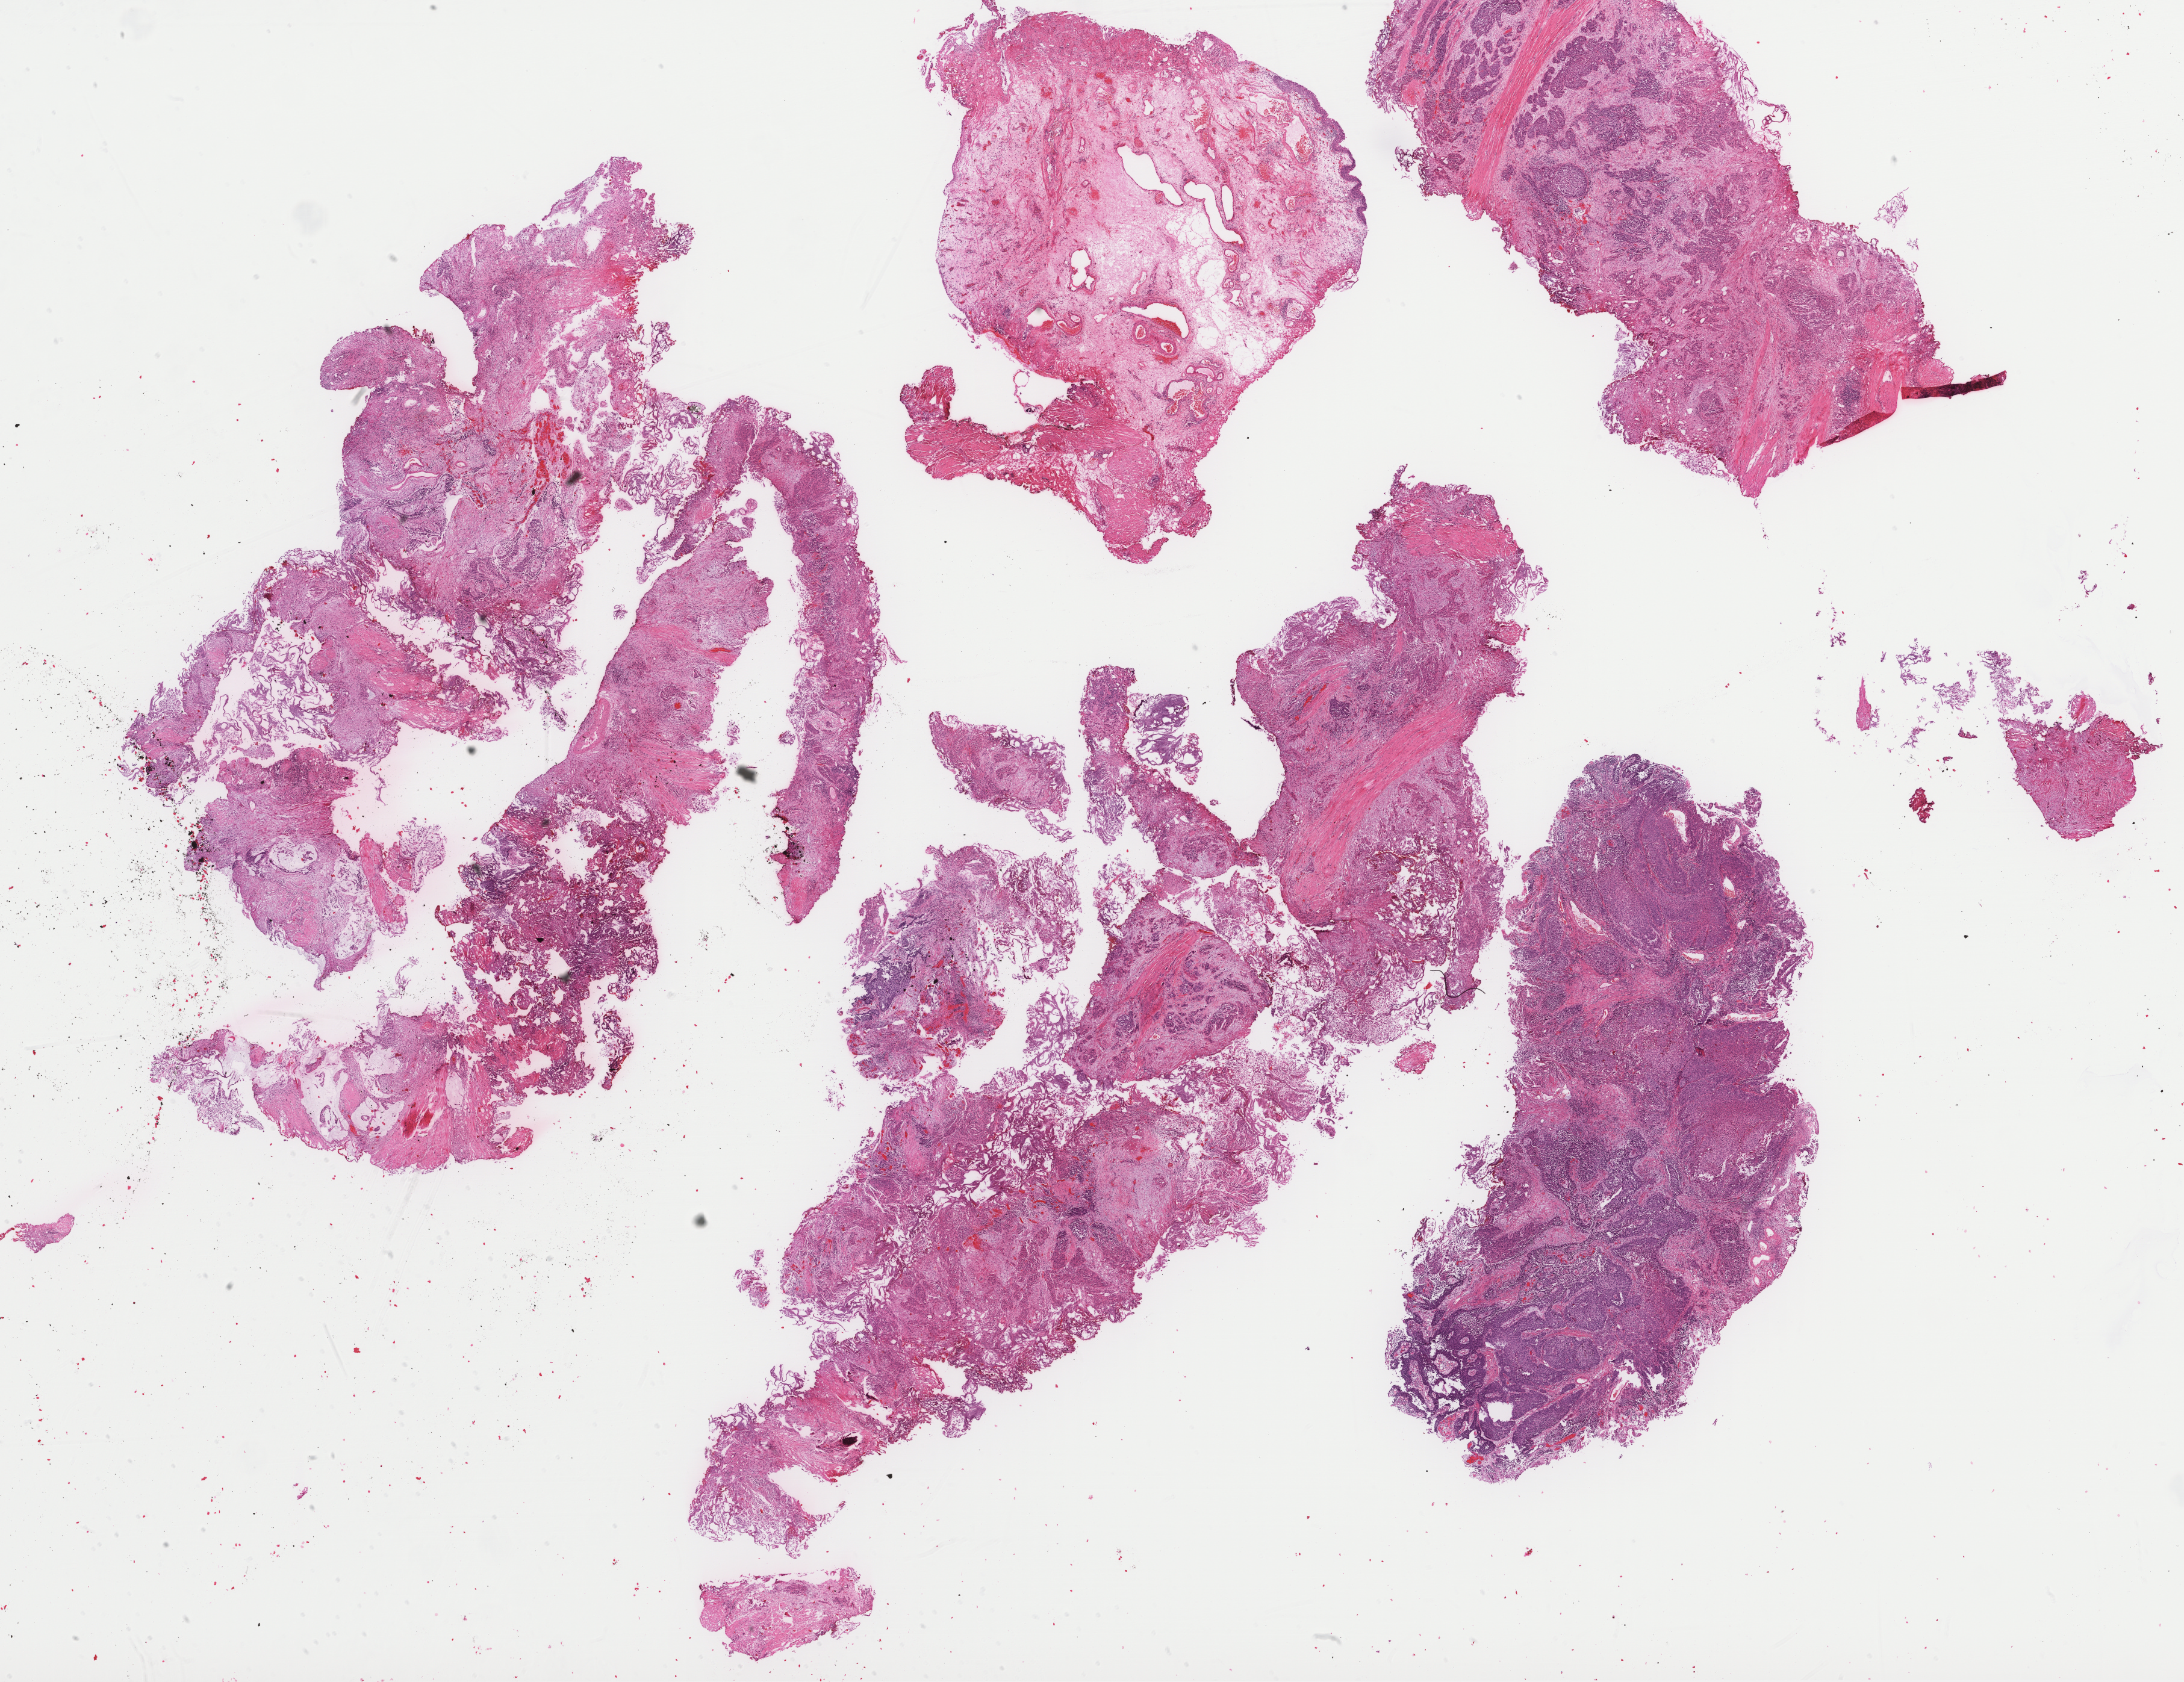
H&E-stained whole-slide image, low-resolution overview of the scanned area, about 29.4 x 22.7 mm, formalin-fixed paraffin-embedded (FFPE) diagnostic section, sample: primary tumour, bladder. Patient: female, age at initial diagnosis 64 years. Histologic grade: high grade.
Diagnosis: Transitional cell carcinoma. AJCC pathologic stage: IV (7th edition).